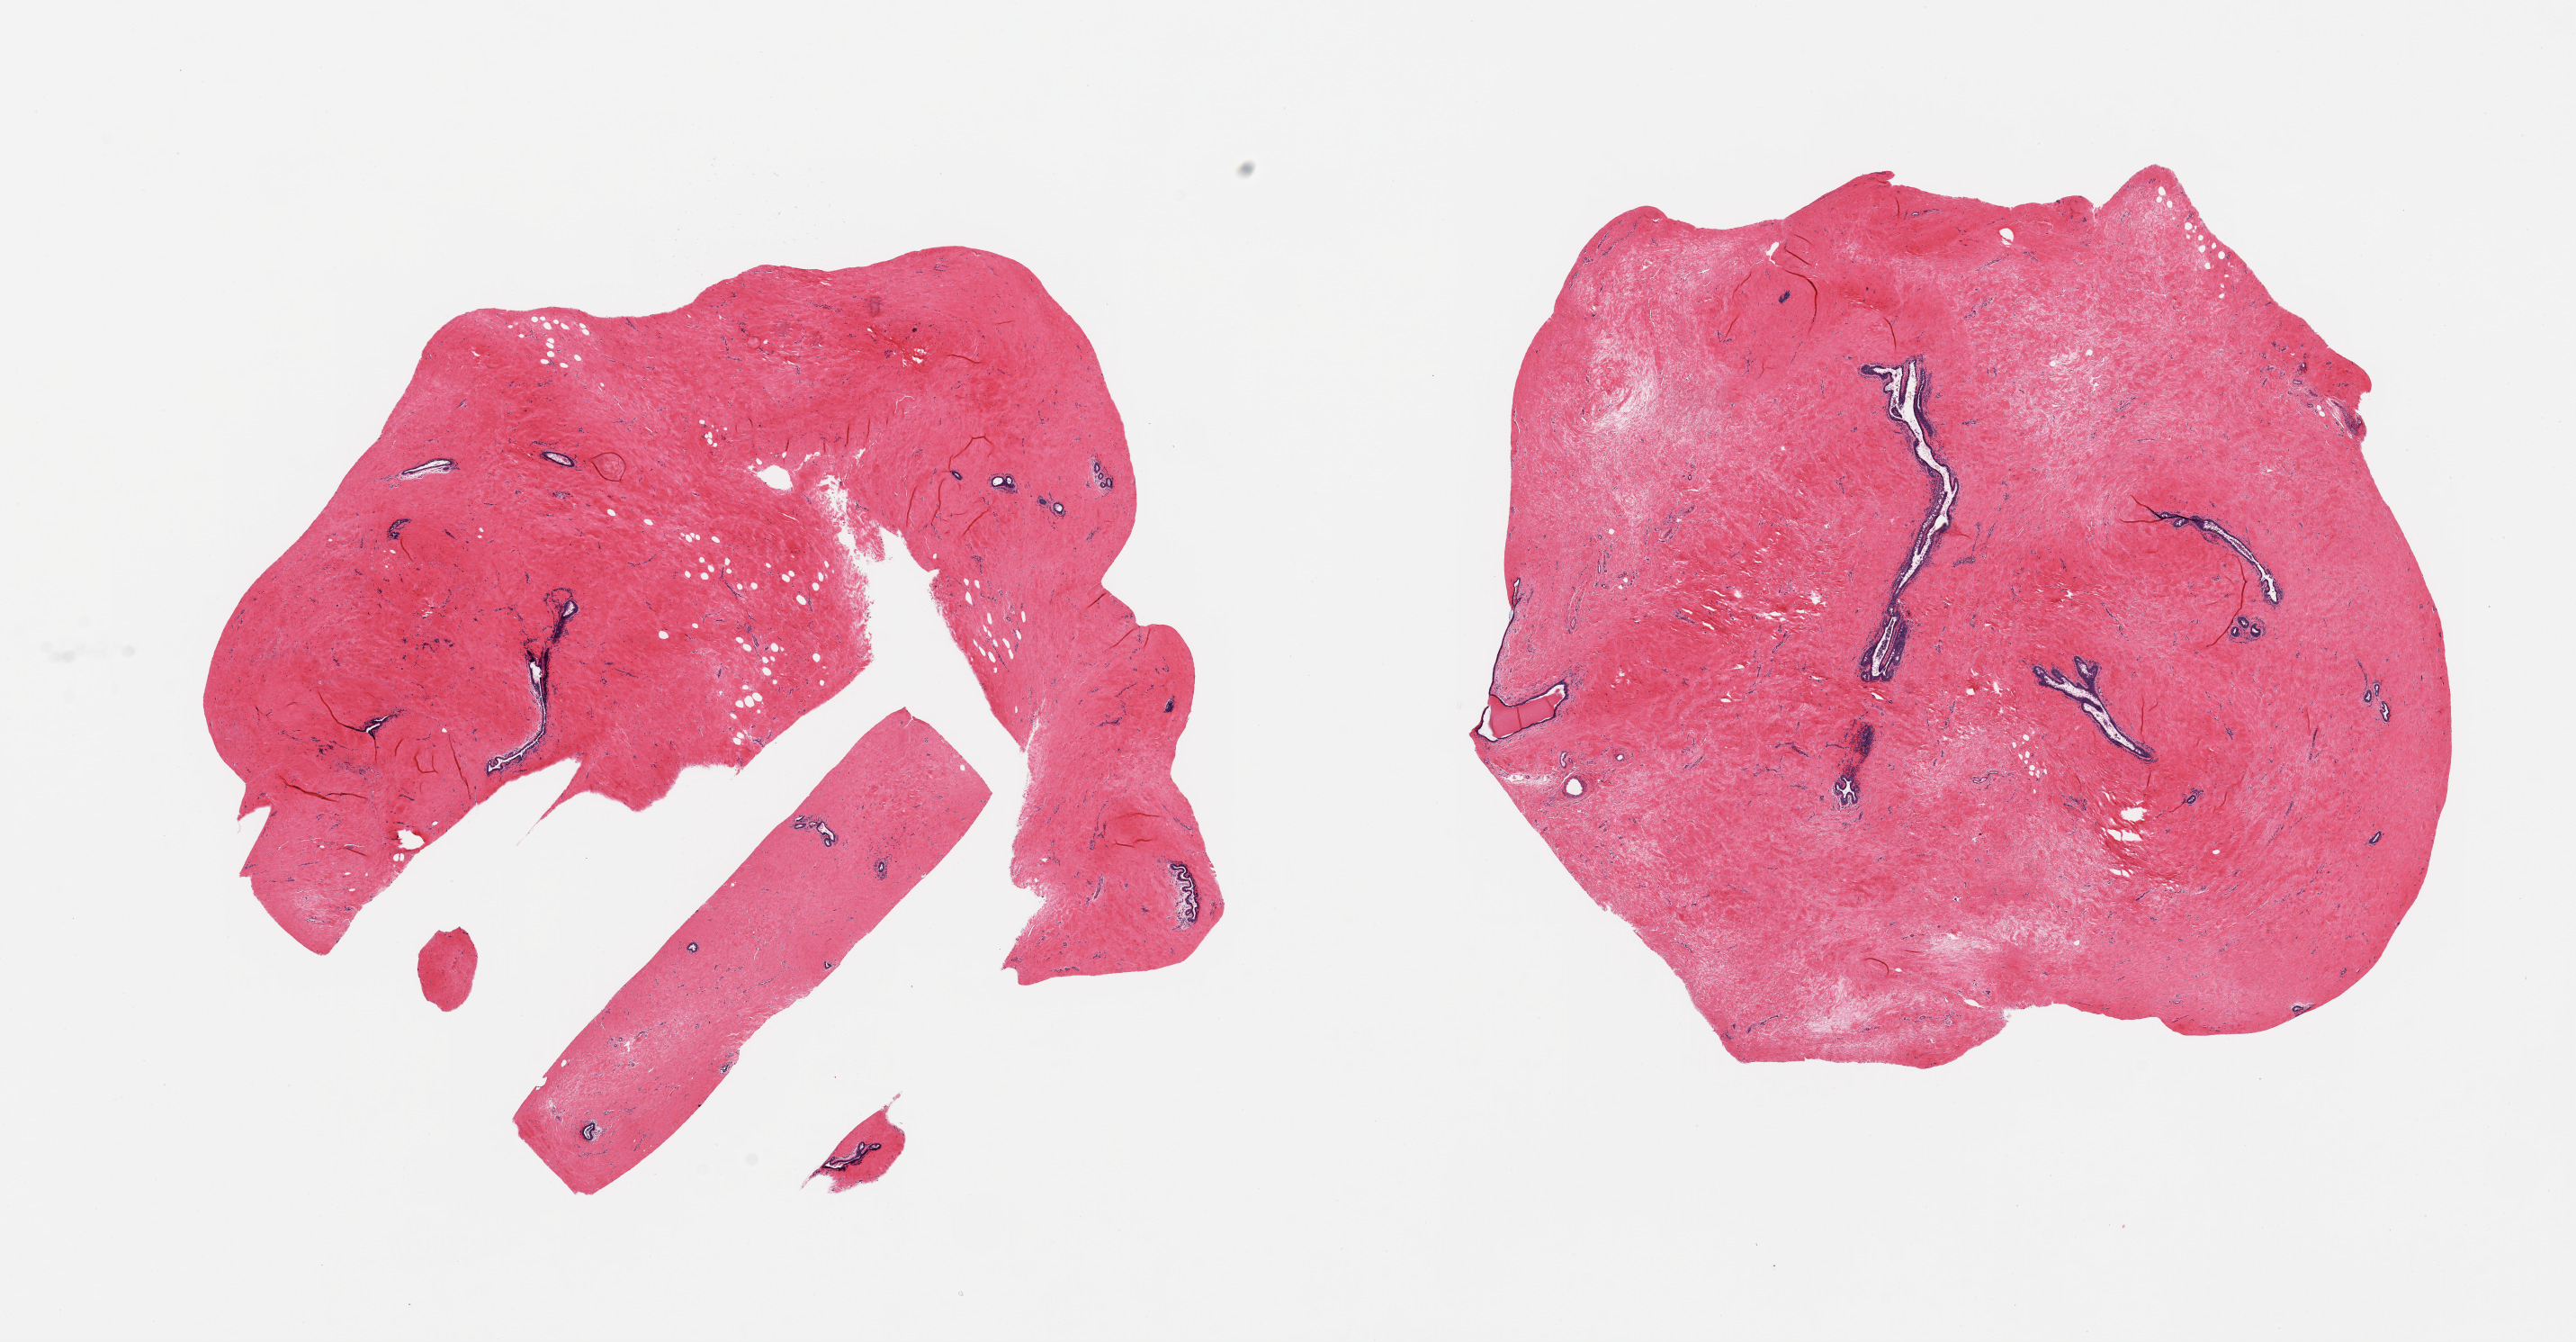
Whole-slide image, H&E stain, brightfield, whole scanned area (about 22.6 x 11.8 mm, from a 20x scan) shown as a low-resolution overview; PAXgene-fixed paraffin-embedded (PFPE) section; sampled site (target tissue): breast; donor tissue sample. Donor sex: male.
• review note (as recorded): 2 pieces (fragmented); dense fibrous stroma and ducts with features of gynecomastia